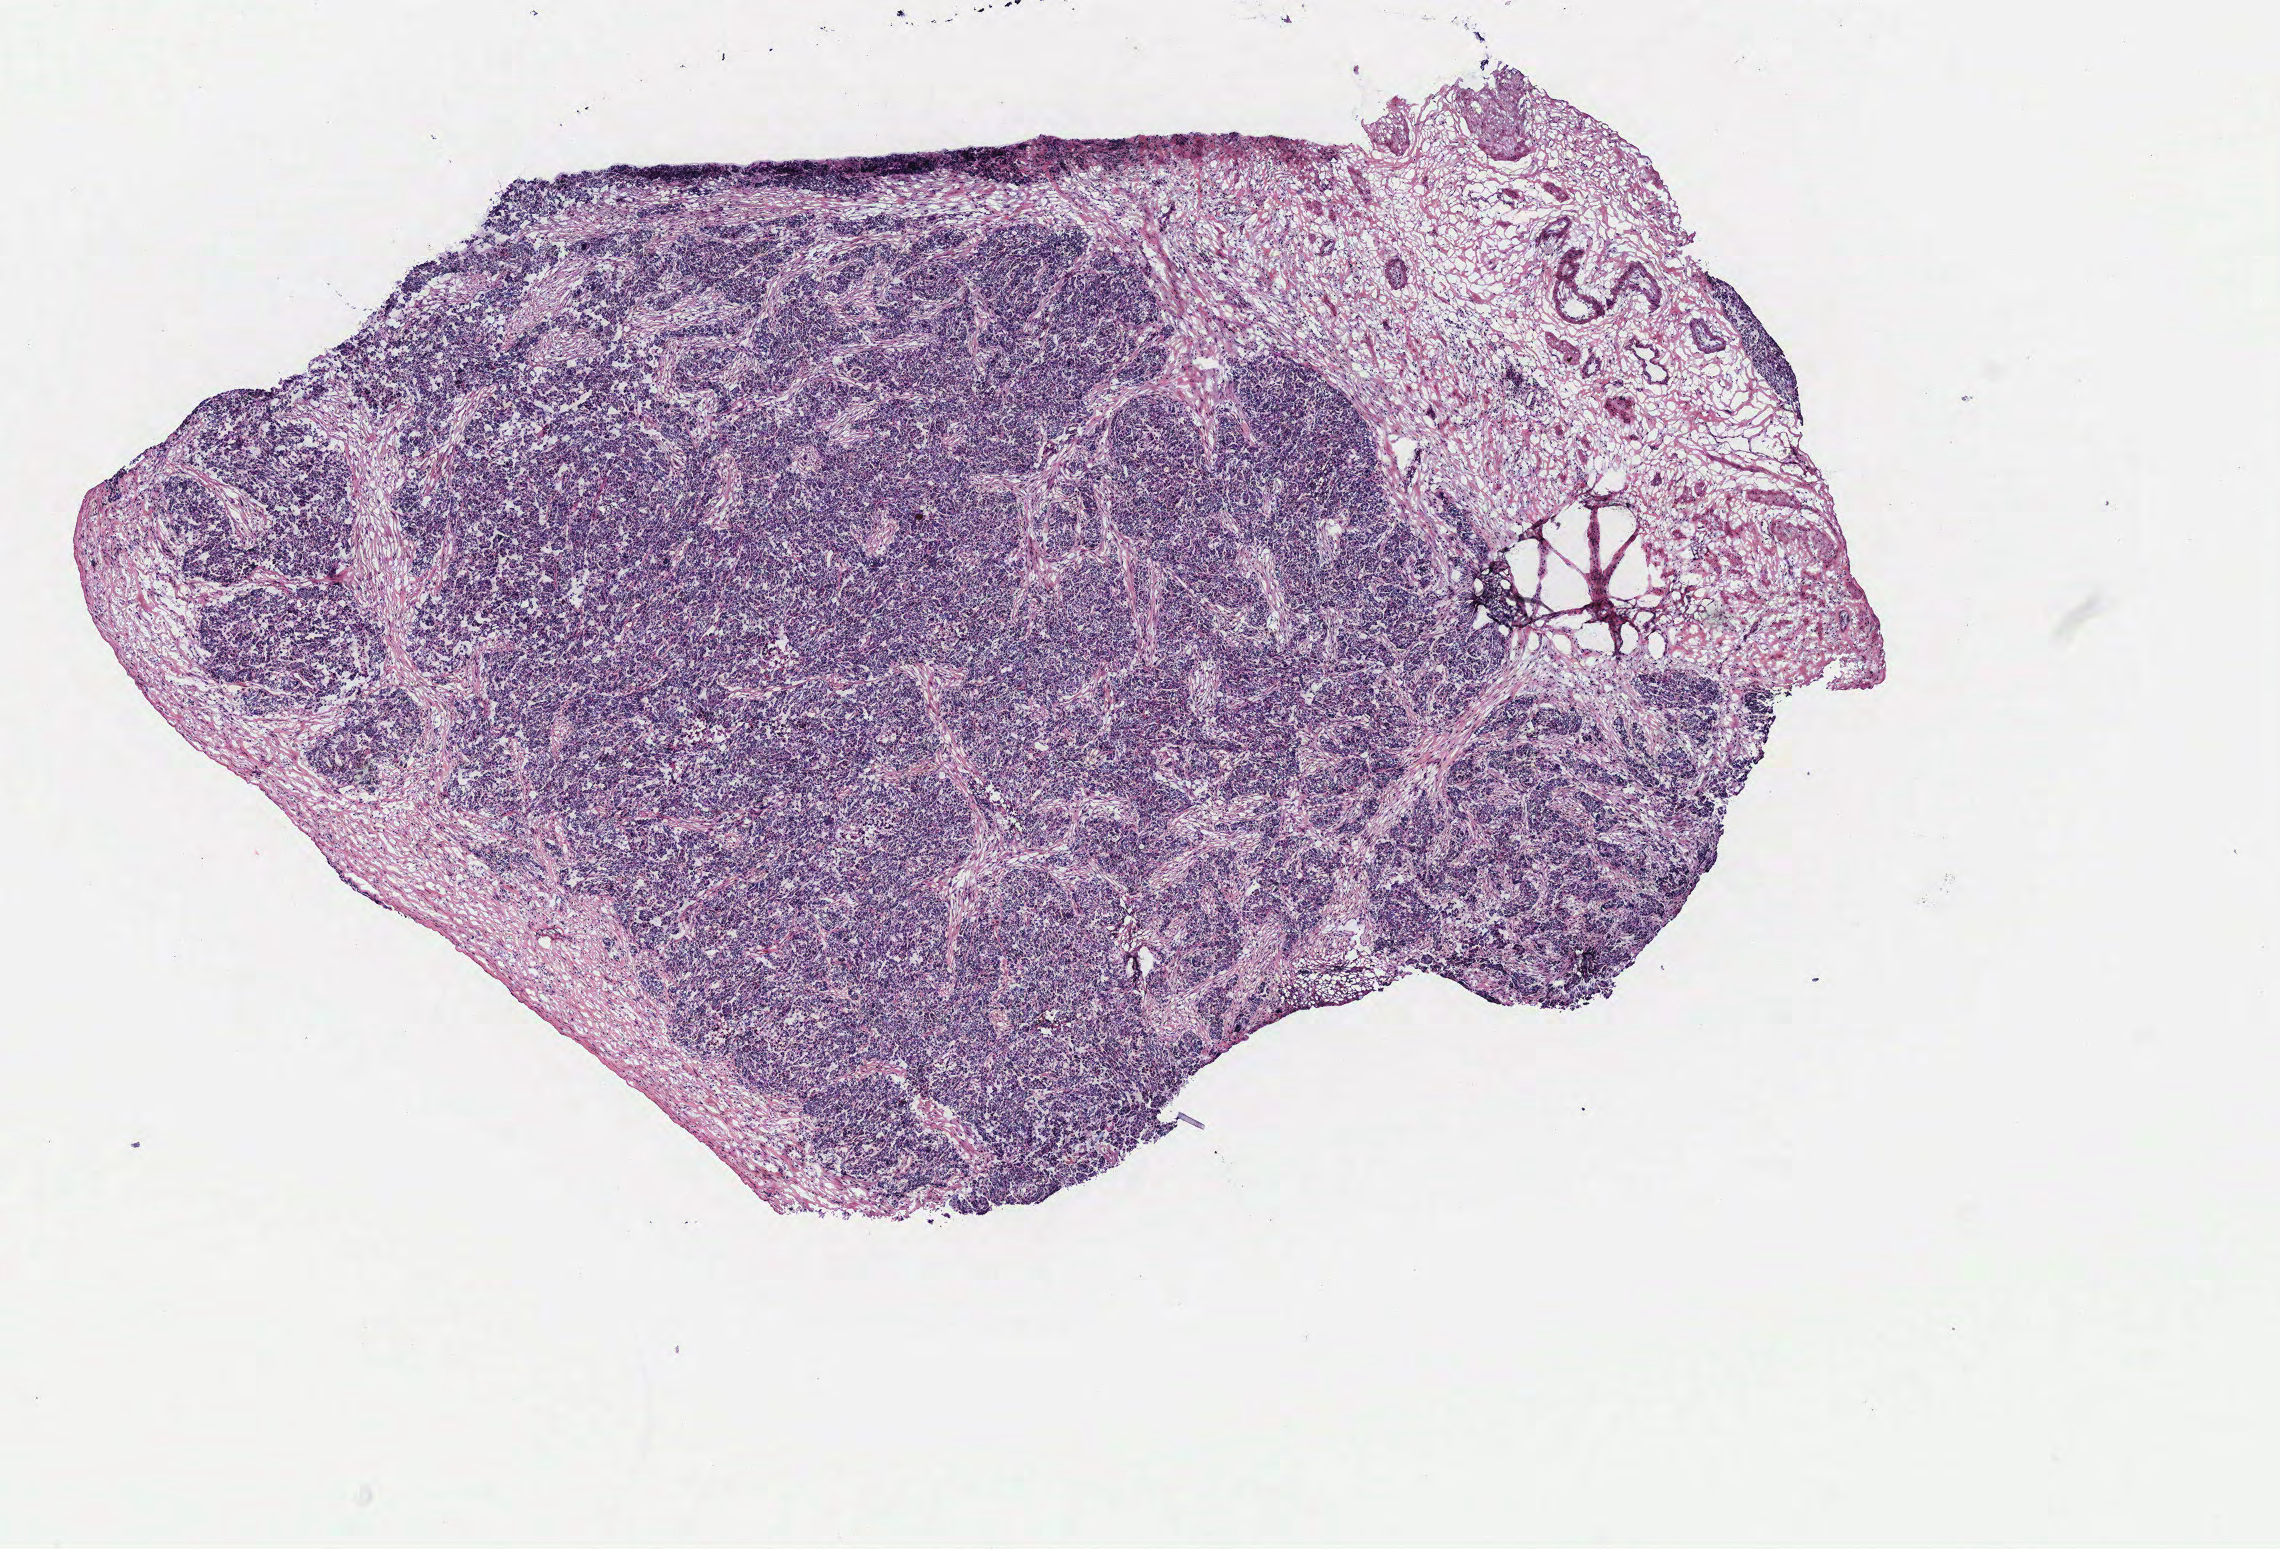
H&E whole-slide image, a low-resolution overview of the entire scanned area, about 9.1 x 6.2 mm, tumour tissue sample, ovary. Female, 77 y/o.
* primary tumour site (as recorded): ovary
* histologic diagnosis: Serous adenocarcinoma, NOS